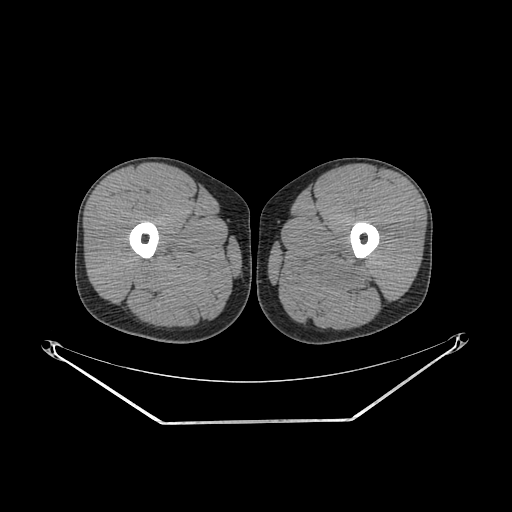
CT of an extremity soft-tissue mass (from a PET/CT study), one axial slice; position 240 of 267 along the scan axis; 140 kVp; soft-tissue window (W 400 / L 40 HU); 3.75 mm slice thickness; 512 × 512 image matrix. Male patient. From the clinical record (not read from this slice): histological type: extraskeletal osteosarcoma; grade: high; site of the primary tumour: left adductur.
Structures marked on this image (expert contour drawn on MRI and transferred to this co-registered scan by the dataset authors):
- gross tumour volume (mass): bounding box [x1, y1, x2, y2] px = [283, 247, 380, 300]